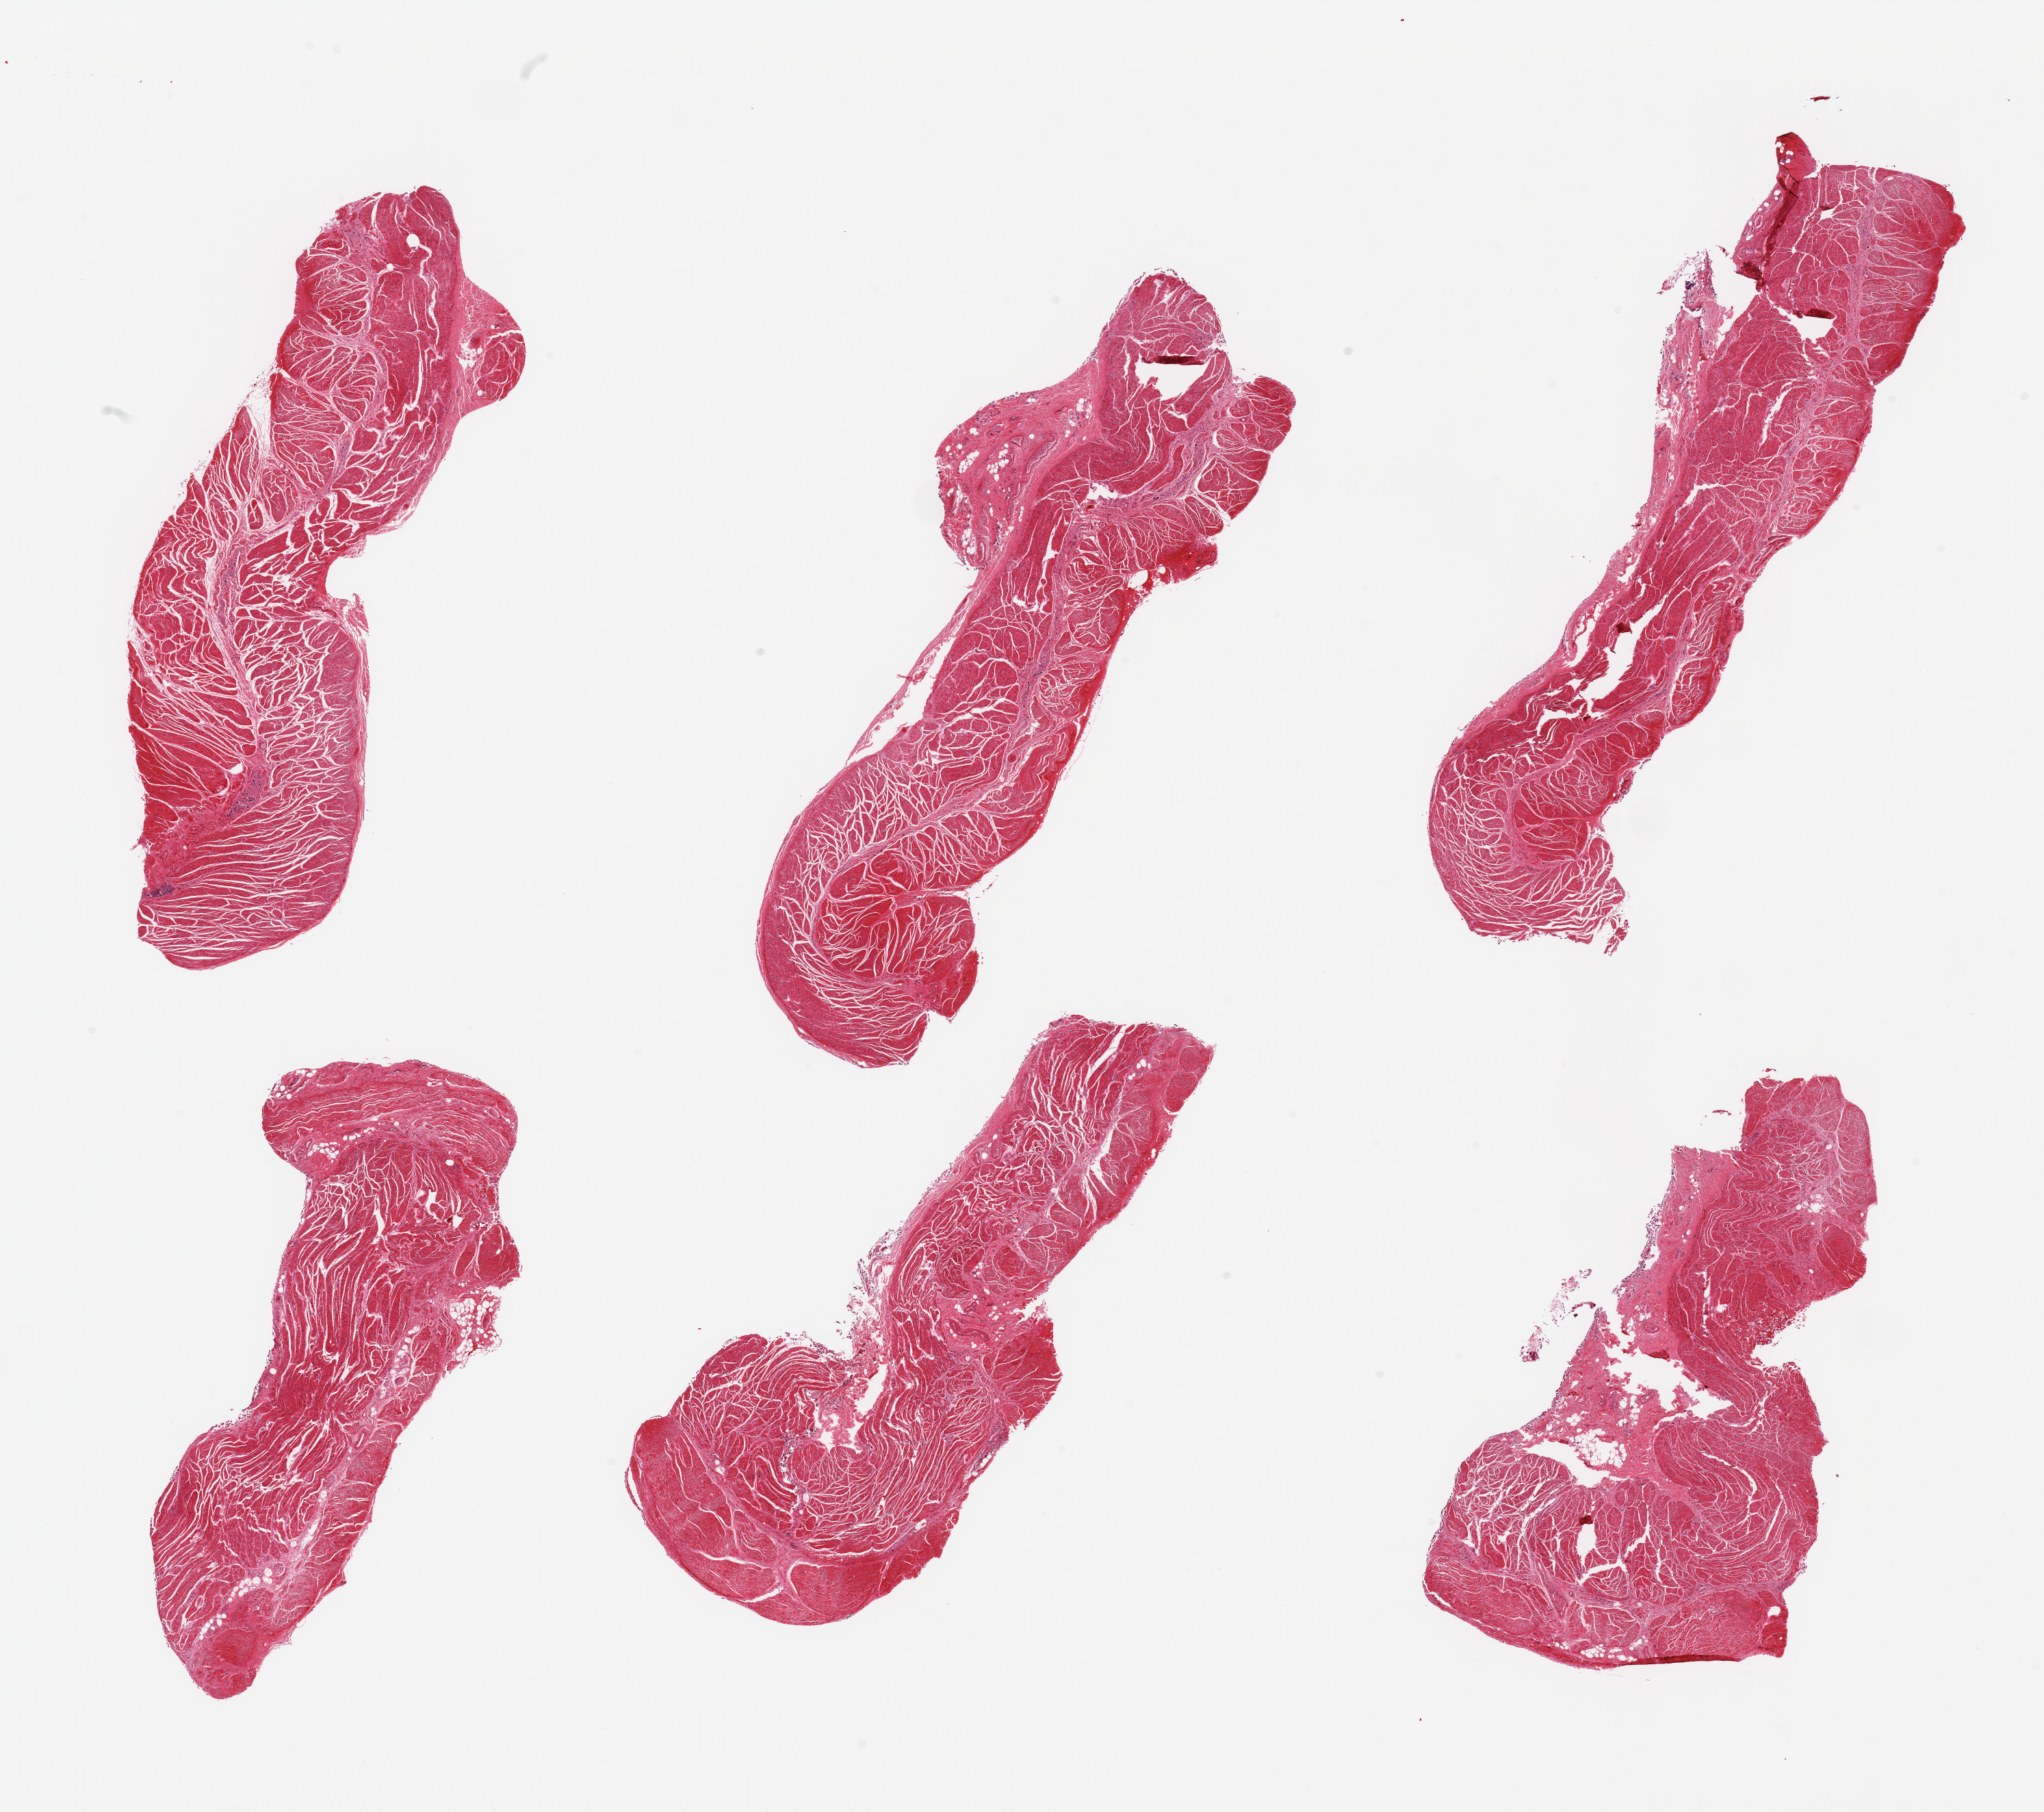
H&E whole-slide image, low-resolution overview of the scanned area, about 23.6 x 20.9 mm (from a 20x scan), PAXgene-fixed paraffin-embedded (PFPE) section, target tissue: esophageal muscle, tissue donor sample. Donor: male.
• pathologist's review note for this sample: 6 pieces; predominantly target muscularis, small amount of residual fat/vessels and detached squamous epithelial cells